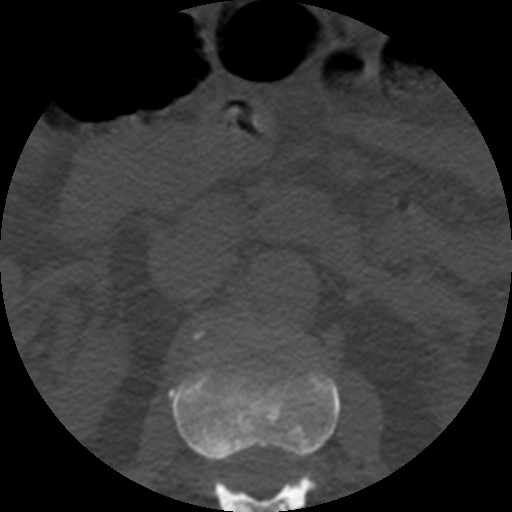
CT including the spine, one axial slice; position 175 of 508 along the scan axis; bone window (W 1800 / L 400 HU); 1.25 mm slice thickness; 512 × 512 image matrix. Patient age 57 years. From the clinical record (not read from this slice): primary cancer: prostate.
Structures marked on this image (semi-automatic segmentation, software-assisted and operator-edited):
- L1 vertebra: bounding box (x1, y1, x2, y2) in pixels: (170, 367, 340, 512)
- L2 vertebra: (195, 334, 199, 339)